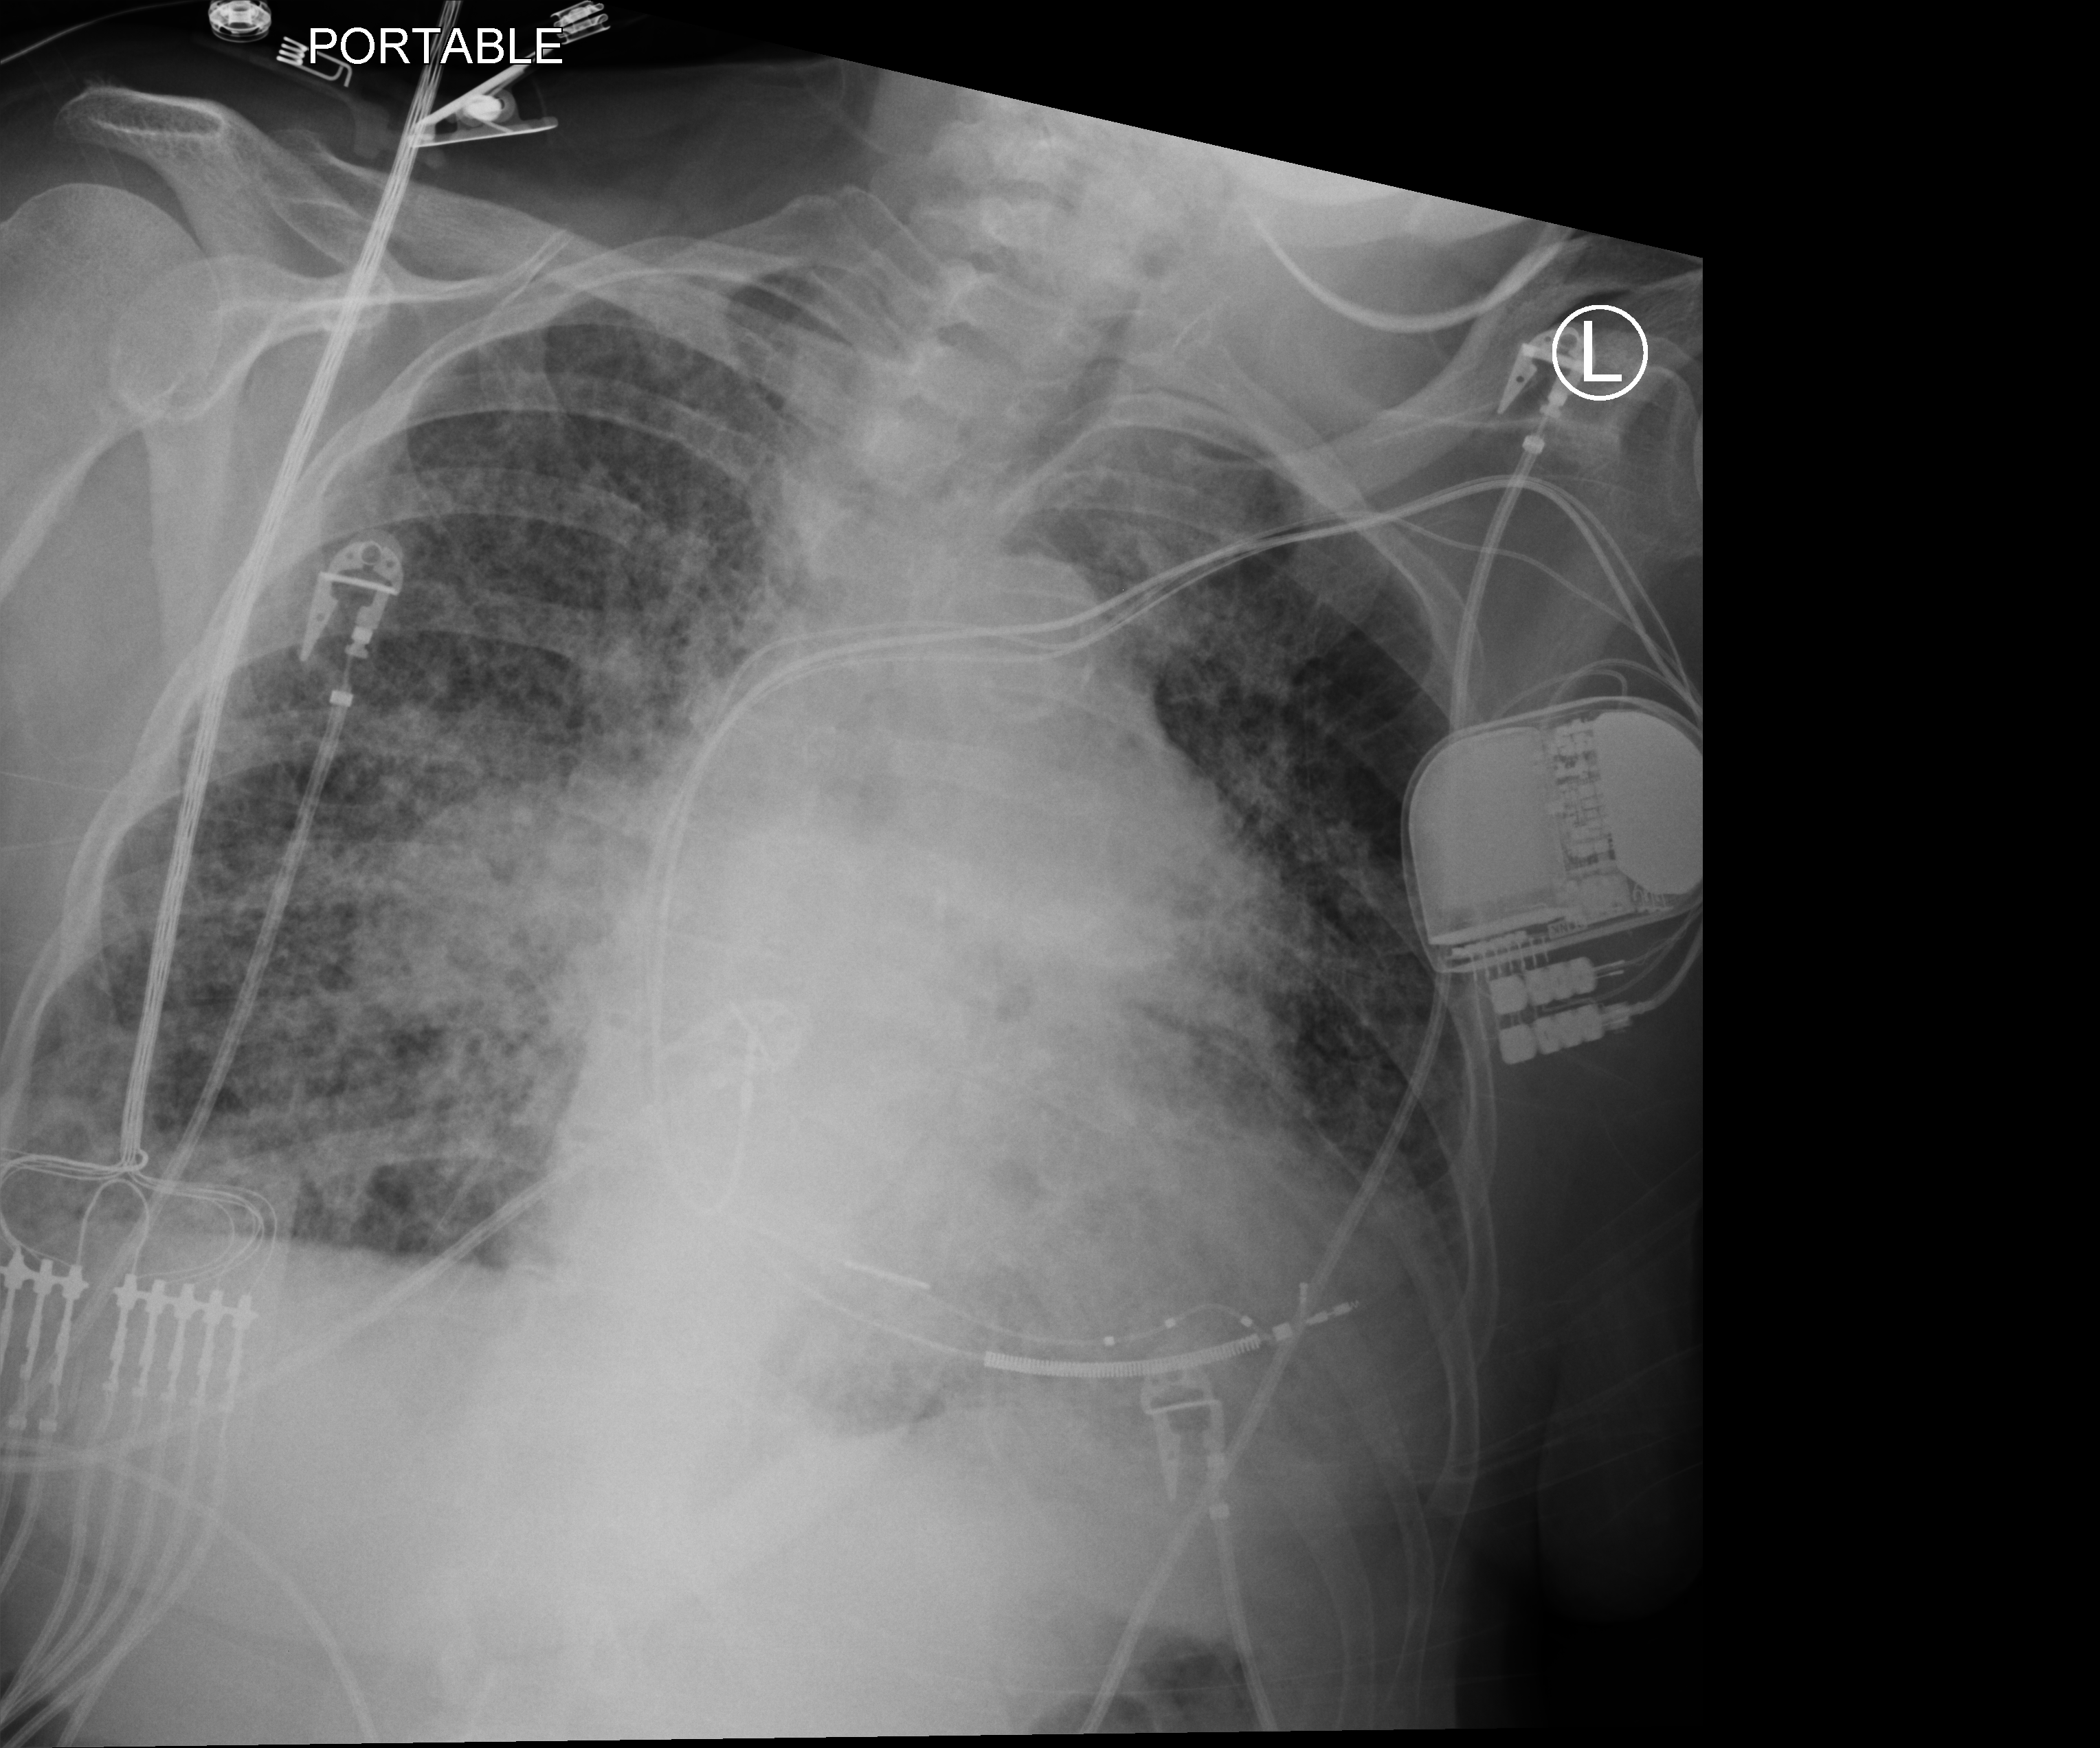
Chest X-ray (portable), anteroposterior (AP) projection. Patient hospitalised with COVID-19; female, aged 60–74 years.
Hospital-stay facts (about this admission, not read from this image; timing relative to this image not recorded):
- admitted to intensive care during this hospital stay: yes
- mechanically ventilated during this hospital stay: no